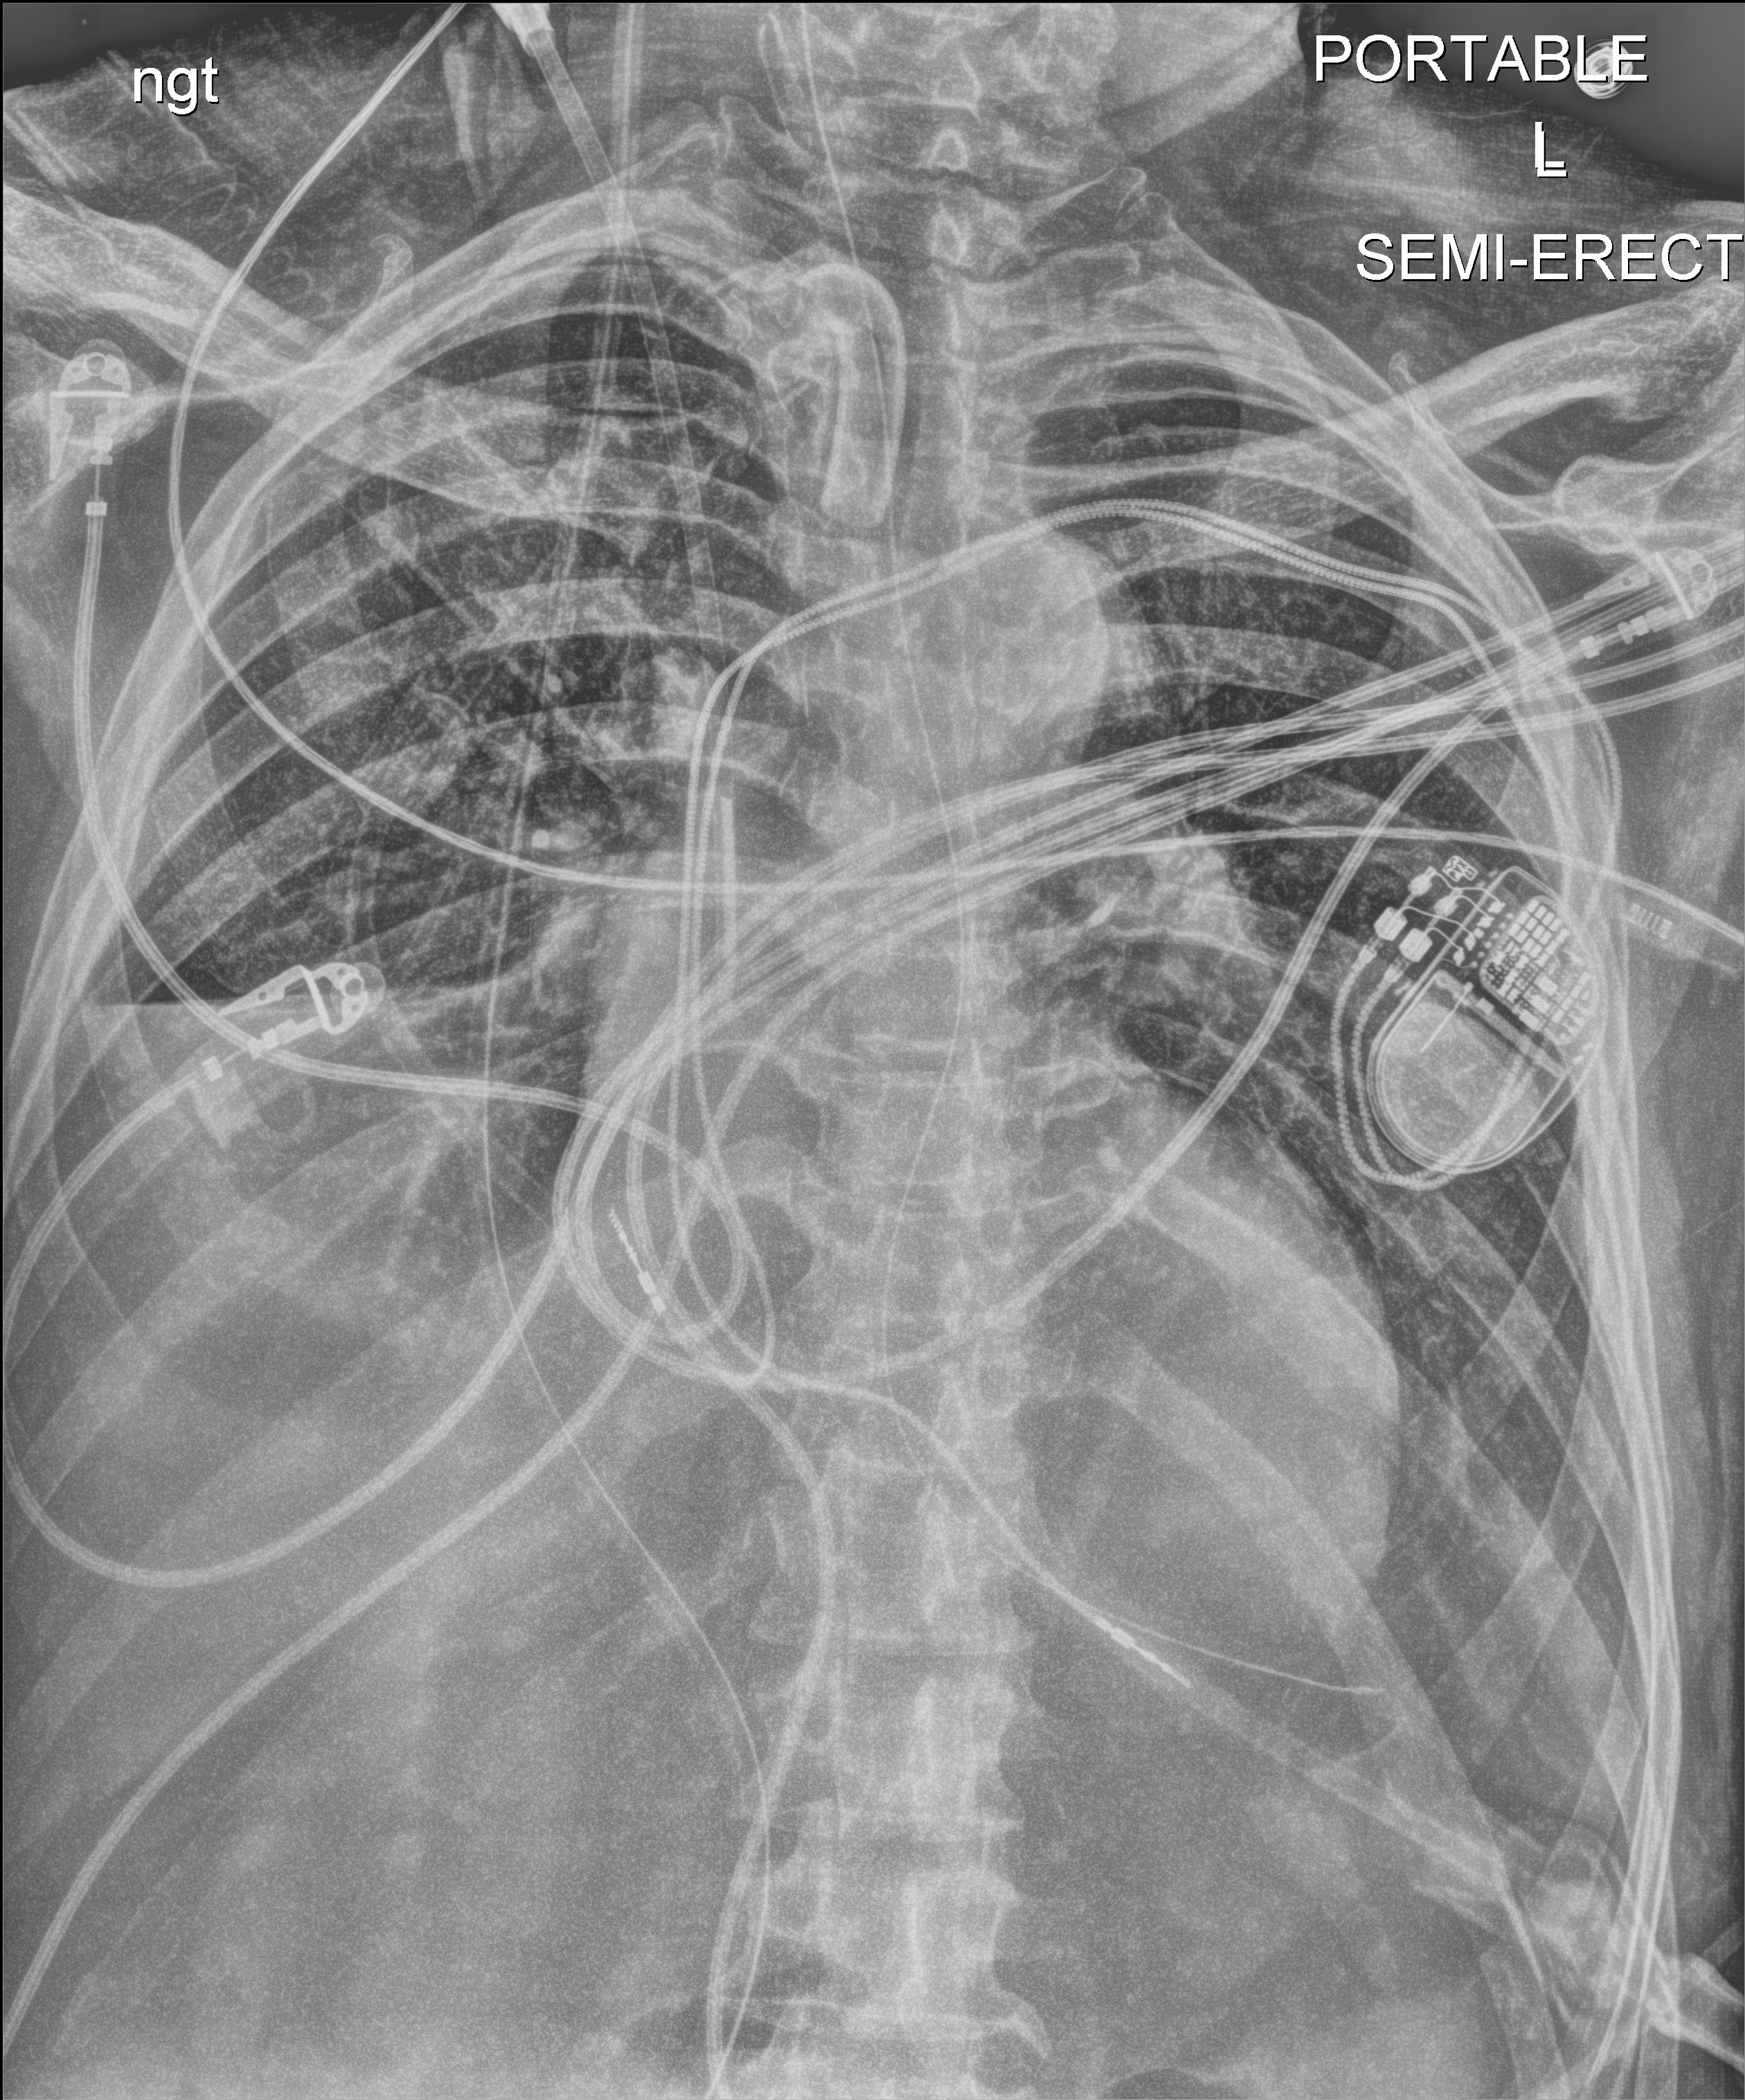
Bedside chest radiograph (digital radiography); anteroposterior (AP) projection. Male patient hospitalised with COVID-19, age 60–74 years.
From the hospital-stay record, not from the radiograph (when in the stay this image was taken is not recorded): admitted to intensive care during this hospital stay: yes; mechanically ventilated during this hospital stay: yes.